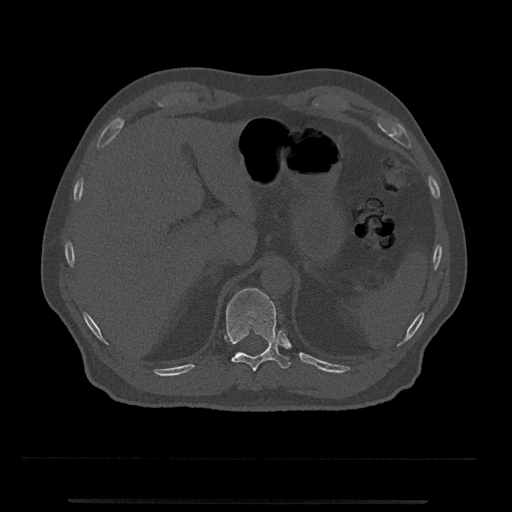
CT including the spine, one axial slice; reconstruction kernel Br40s/3; 120 kVp; bone window (W 1800 / L 400 HU); 512 × 512 image matrix, field of view 419 × 419 mm. Patient: male, 63 years. From the clinical record (not read from this slice): primary cancer: prostate.
Structures marked on this image (semi-automatic segmentation, software-assisted and operator-edited):
- T11 vertebra: bounding box <226,288,291,372> (left, top, right, bottom; pixels)